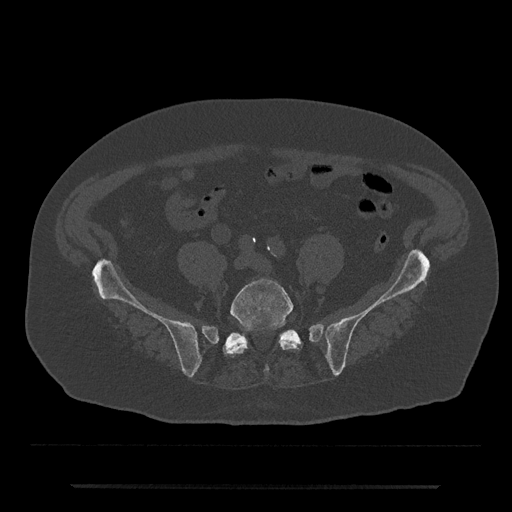
CT including the spine, one axial slice. Position 271 of 797 along the scan axis. Bone window (W 1800 / L 400 HU). 512 × 512 image matrix, field of view 434 × 434 mm. Male patient, age 80 years. Case-level facts recorded for this patient, not image findings: primary cancer: prostate; vertebrae with lytic lesions (as recorded): L1, T11.
Structures marked on this image (semi-automatically segmented with operator editing):
- L5 vertebra: box from (x=223, y=278) to (x=300, y=371) px